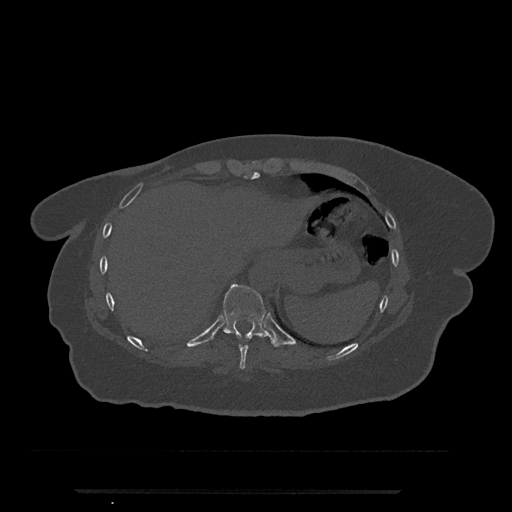
CT including the spine, one axial slice. Slice 306 of 797 in the series (ordered by position). Reconstruction kernel Br40s/3. 120 kVp. Bone window (W 1800 / L 400 HU). 512 × 512 image matrix, field of view 440 × 440 mm. Female patient, age 51 years. Case-level facts recorded for this patient, not image findings: primary cancer: neuro.
Annotated regions visible in this slice (semi-automatic segmentation, software-assisted and operator-edited):
- T10 vertebra: bounding box <223,283,277,347> (left, top, right, bottom; pixels)
- T9 vertebra: <238,344,249,369>